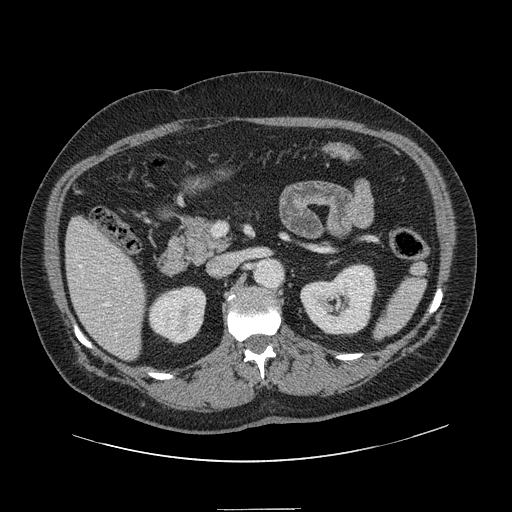
Contrast-enhanced abdominal CT, one axial slice; slice 61 of 154 in the series (ordered by position); 120 kVp; intravenous contrast given; soft-tissue window (W 400 / L 40 HU); 512 × 512 image matrix. Male patient, age 61 years. Case-level facts recorded for this patient, not image findings: diagnosis: colorectal cancer liver metastases, imaged before liver resection; multiple liver metastases: yes; largest metastasis: 2.6 cm.
Structures marked on this image (manually delineated by an expert):
- hepatic veins: box from (x=79, y=265) to (x=117, y=336) px
- liver: (x=67, y=219)–(x=146, y=359)
- planned liver remnant (the part of the liver to remain after resection): (x=67, y=218)–(x=146, y=359)